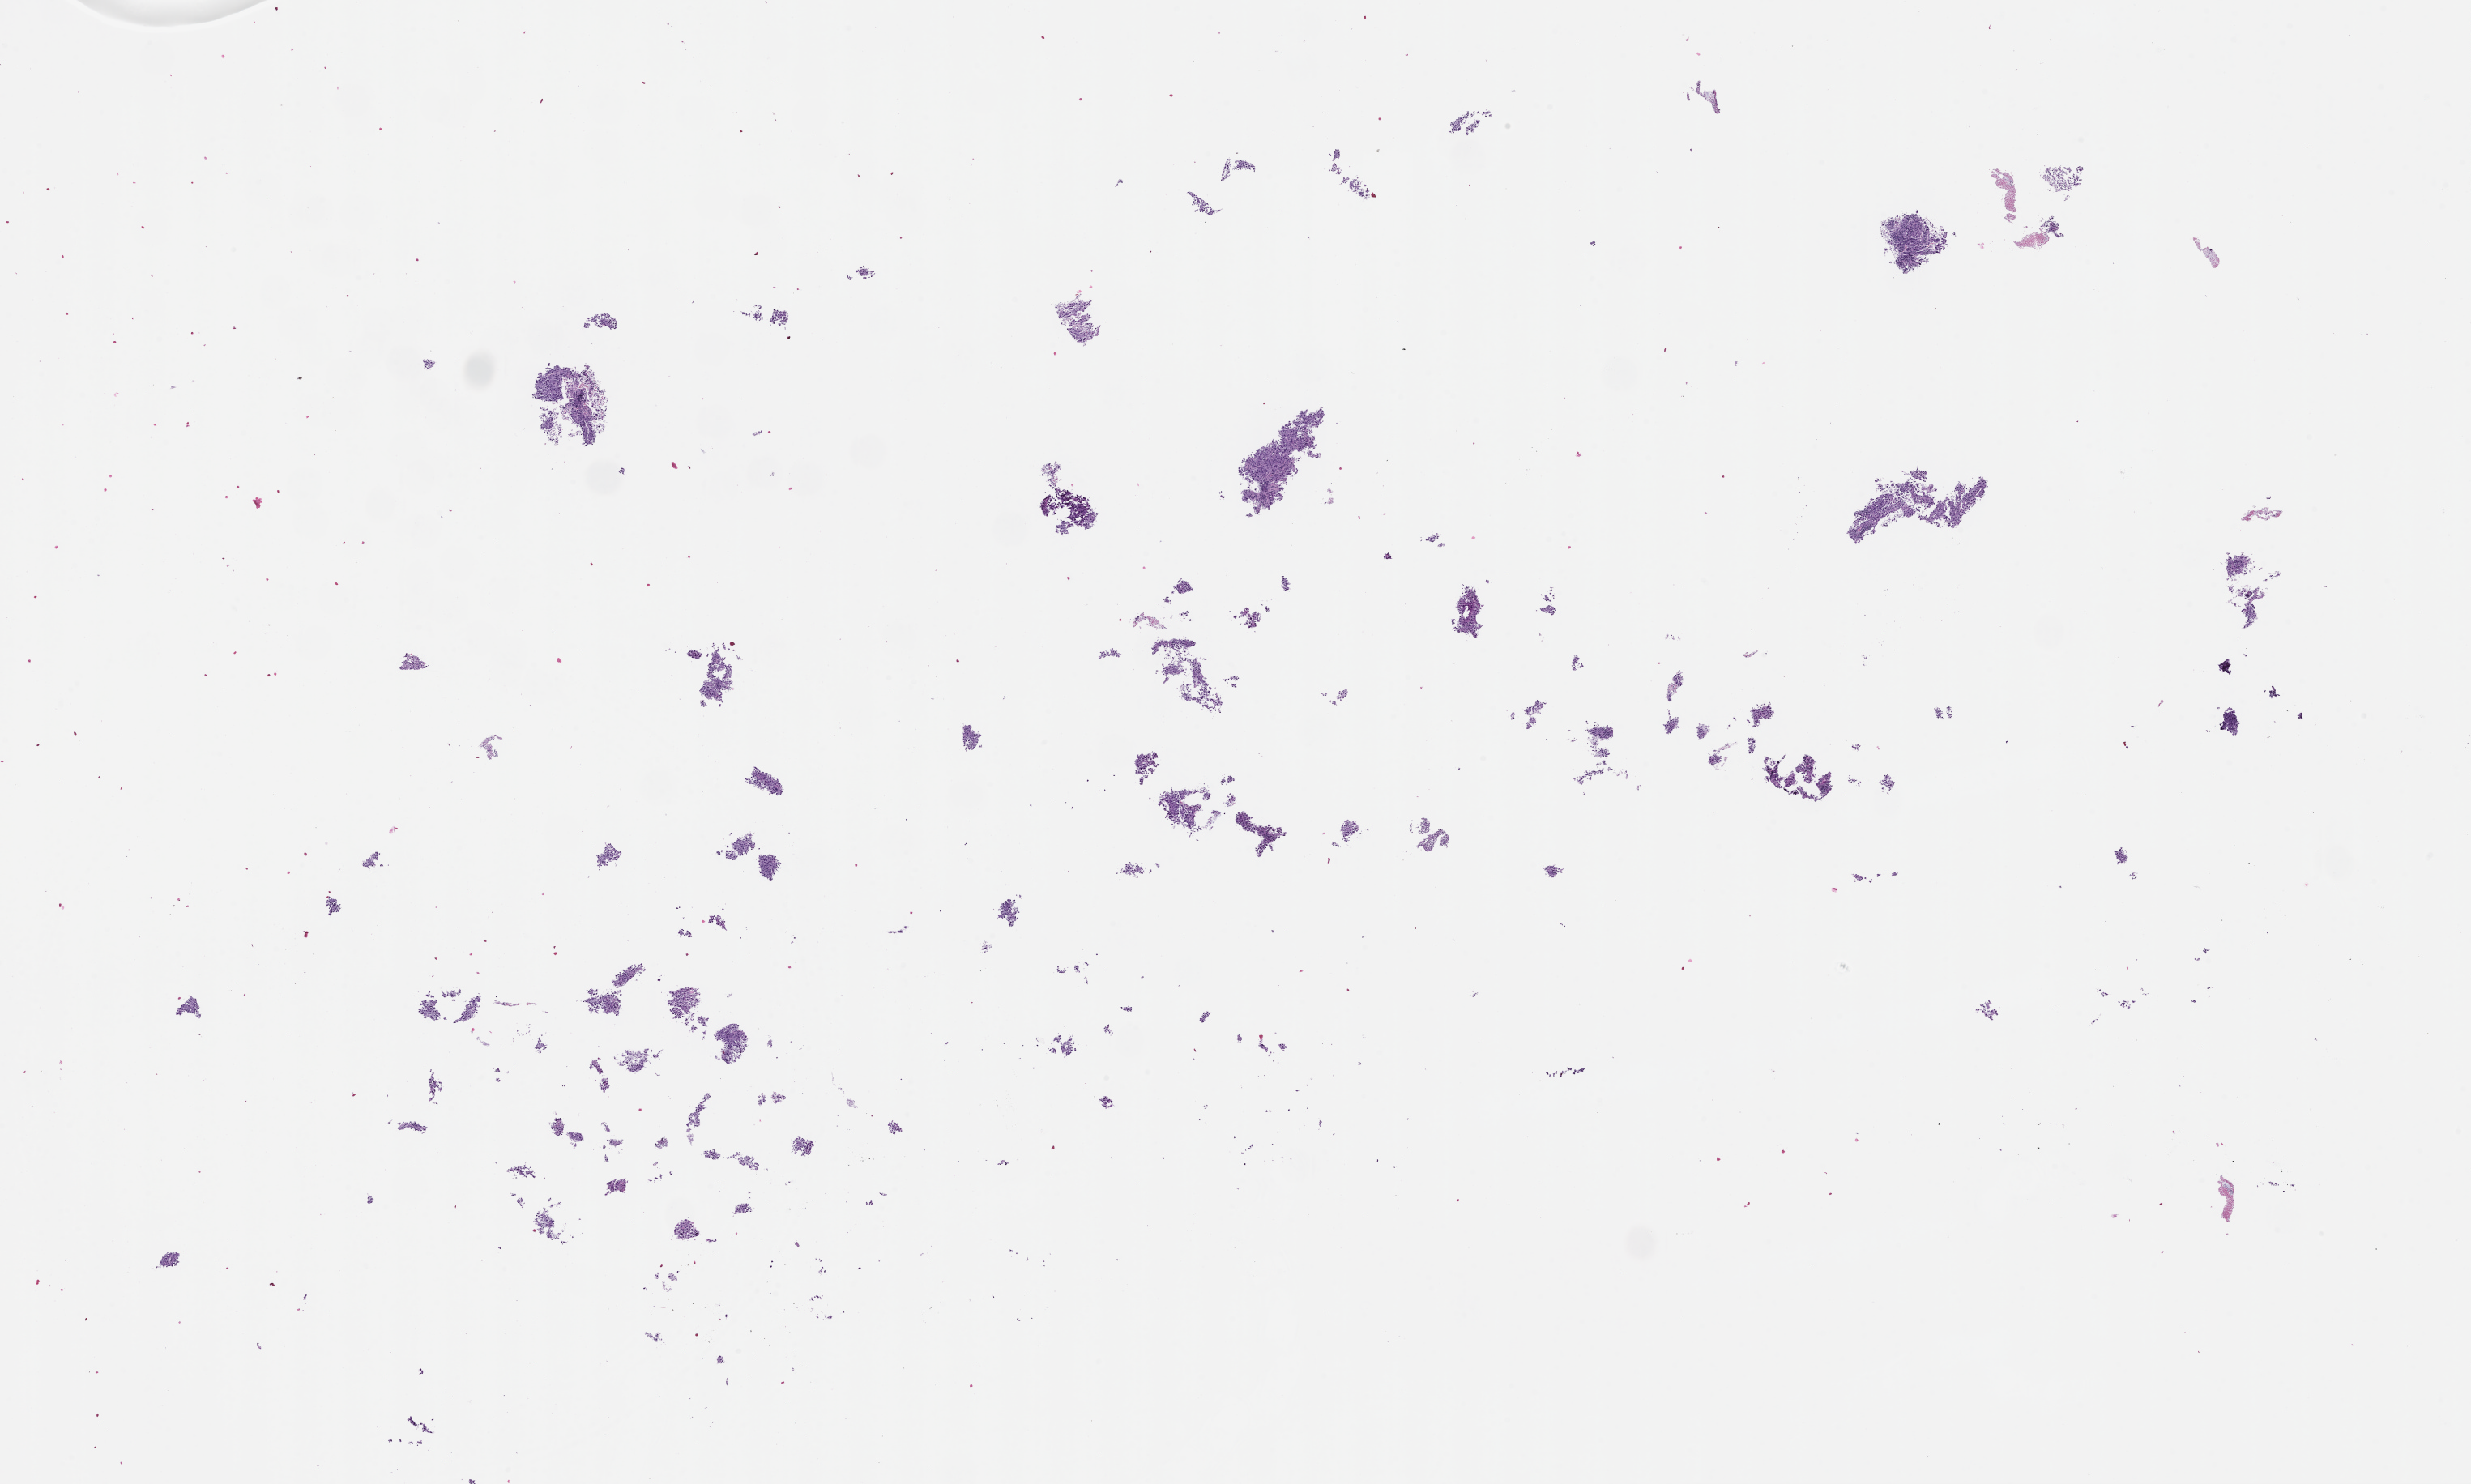
Whole-slide image, hematoxylin and eosin (H&E) stain, shown as a low-resolution overview of the whole scanned area (about 24.6 x 14.8 mm), FFPE section, tissue site: lung. Male patient.
This section: primary tumour tissue. Diagnosis: Non-Small Cell Lung Carcinoma.